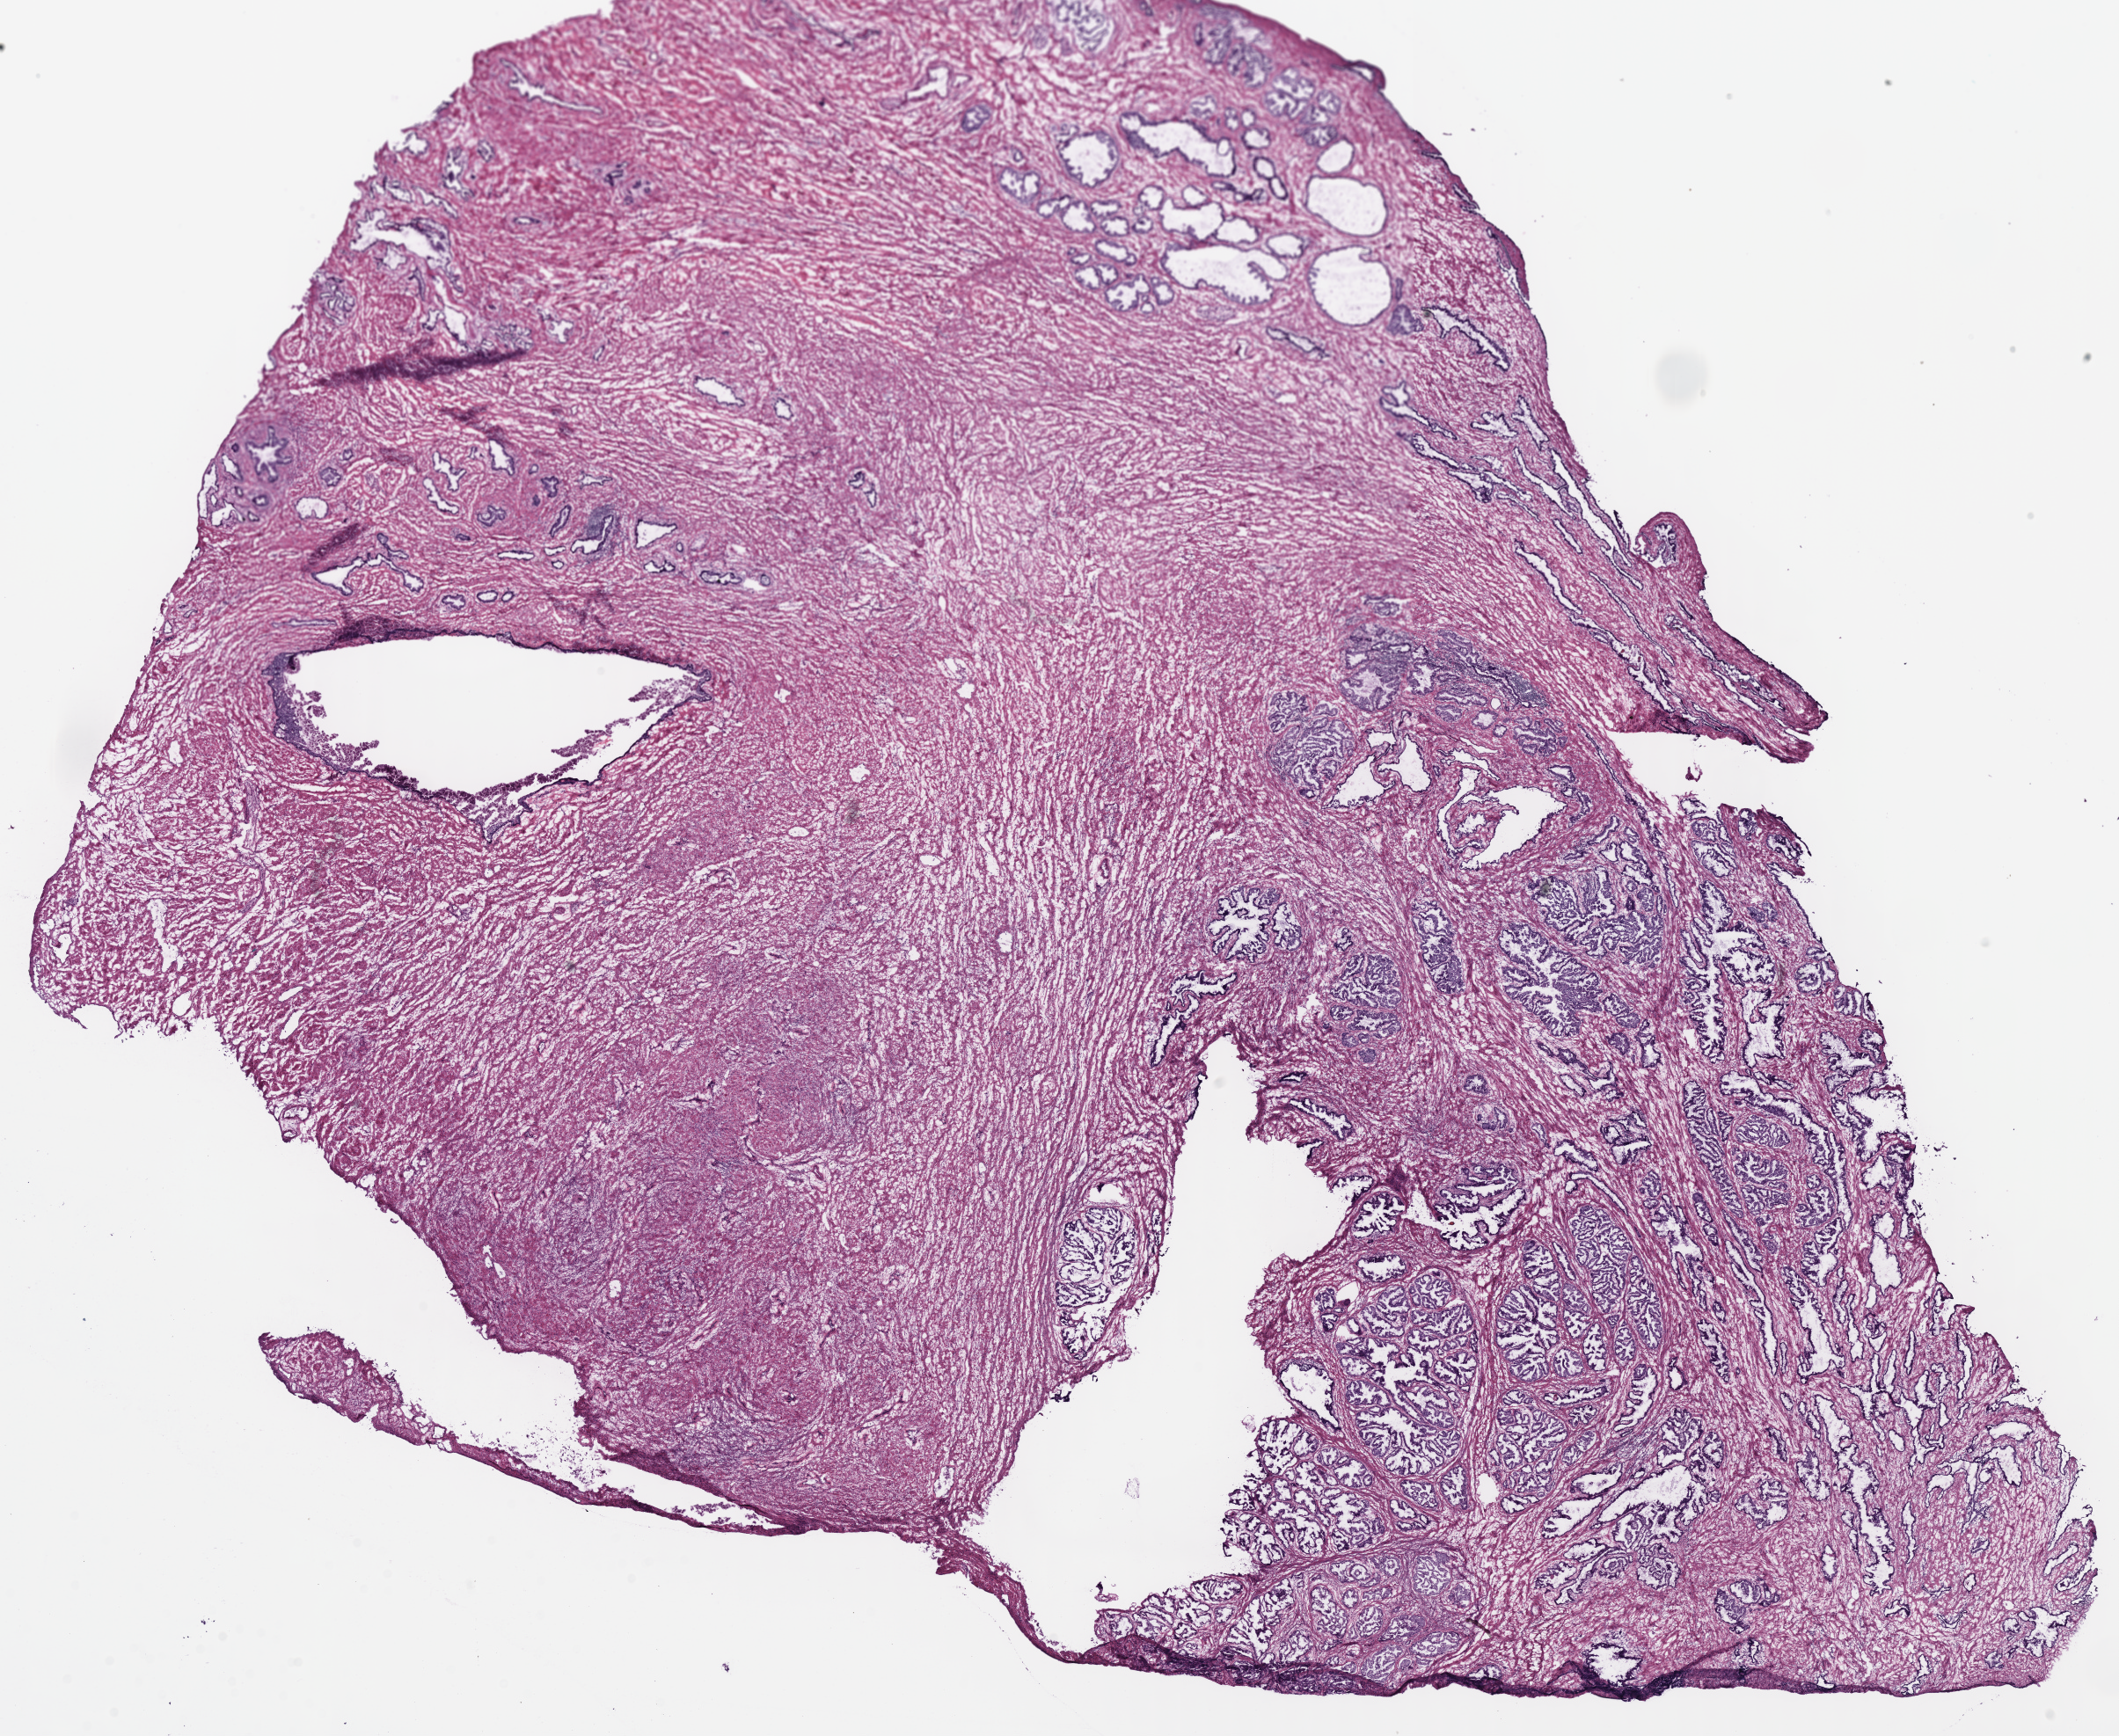
Digitized H&E-stained tissue section (whole slide) — whole scanned area (about 19.0 x 15.6 mm, from a 40x scan) shown as a low-resolution overview. Frozen section from the top of the tissue portion. Prostate, solid tissue normal (non-tumour tissue) sample. Patient: male, age at initial diagnosis 70 years.
This section: solid tissue normal sample (biorepository sample class). Patient diagnosis: Acinar cell carcinoma (prostate gland).